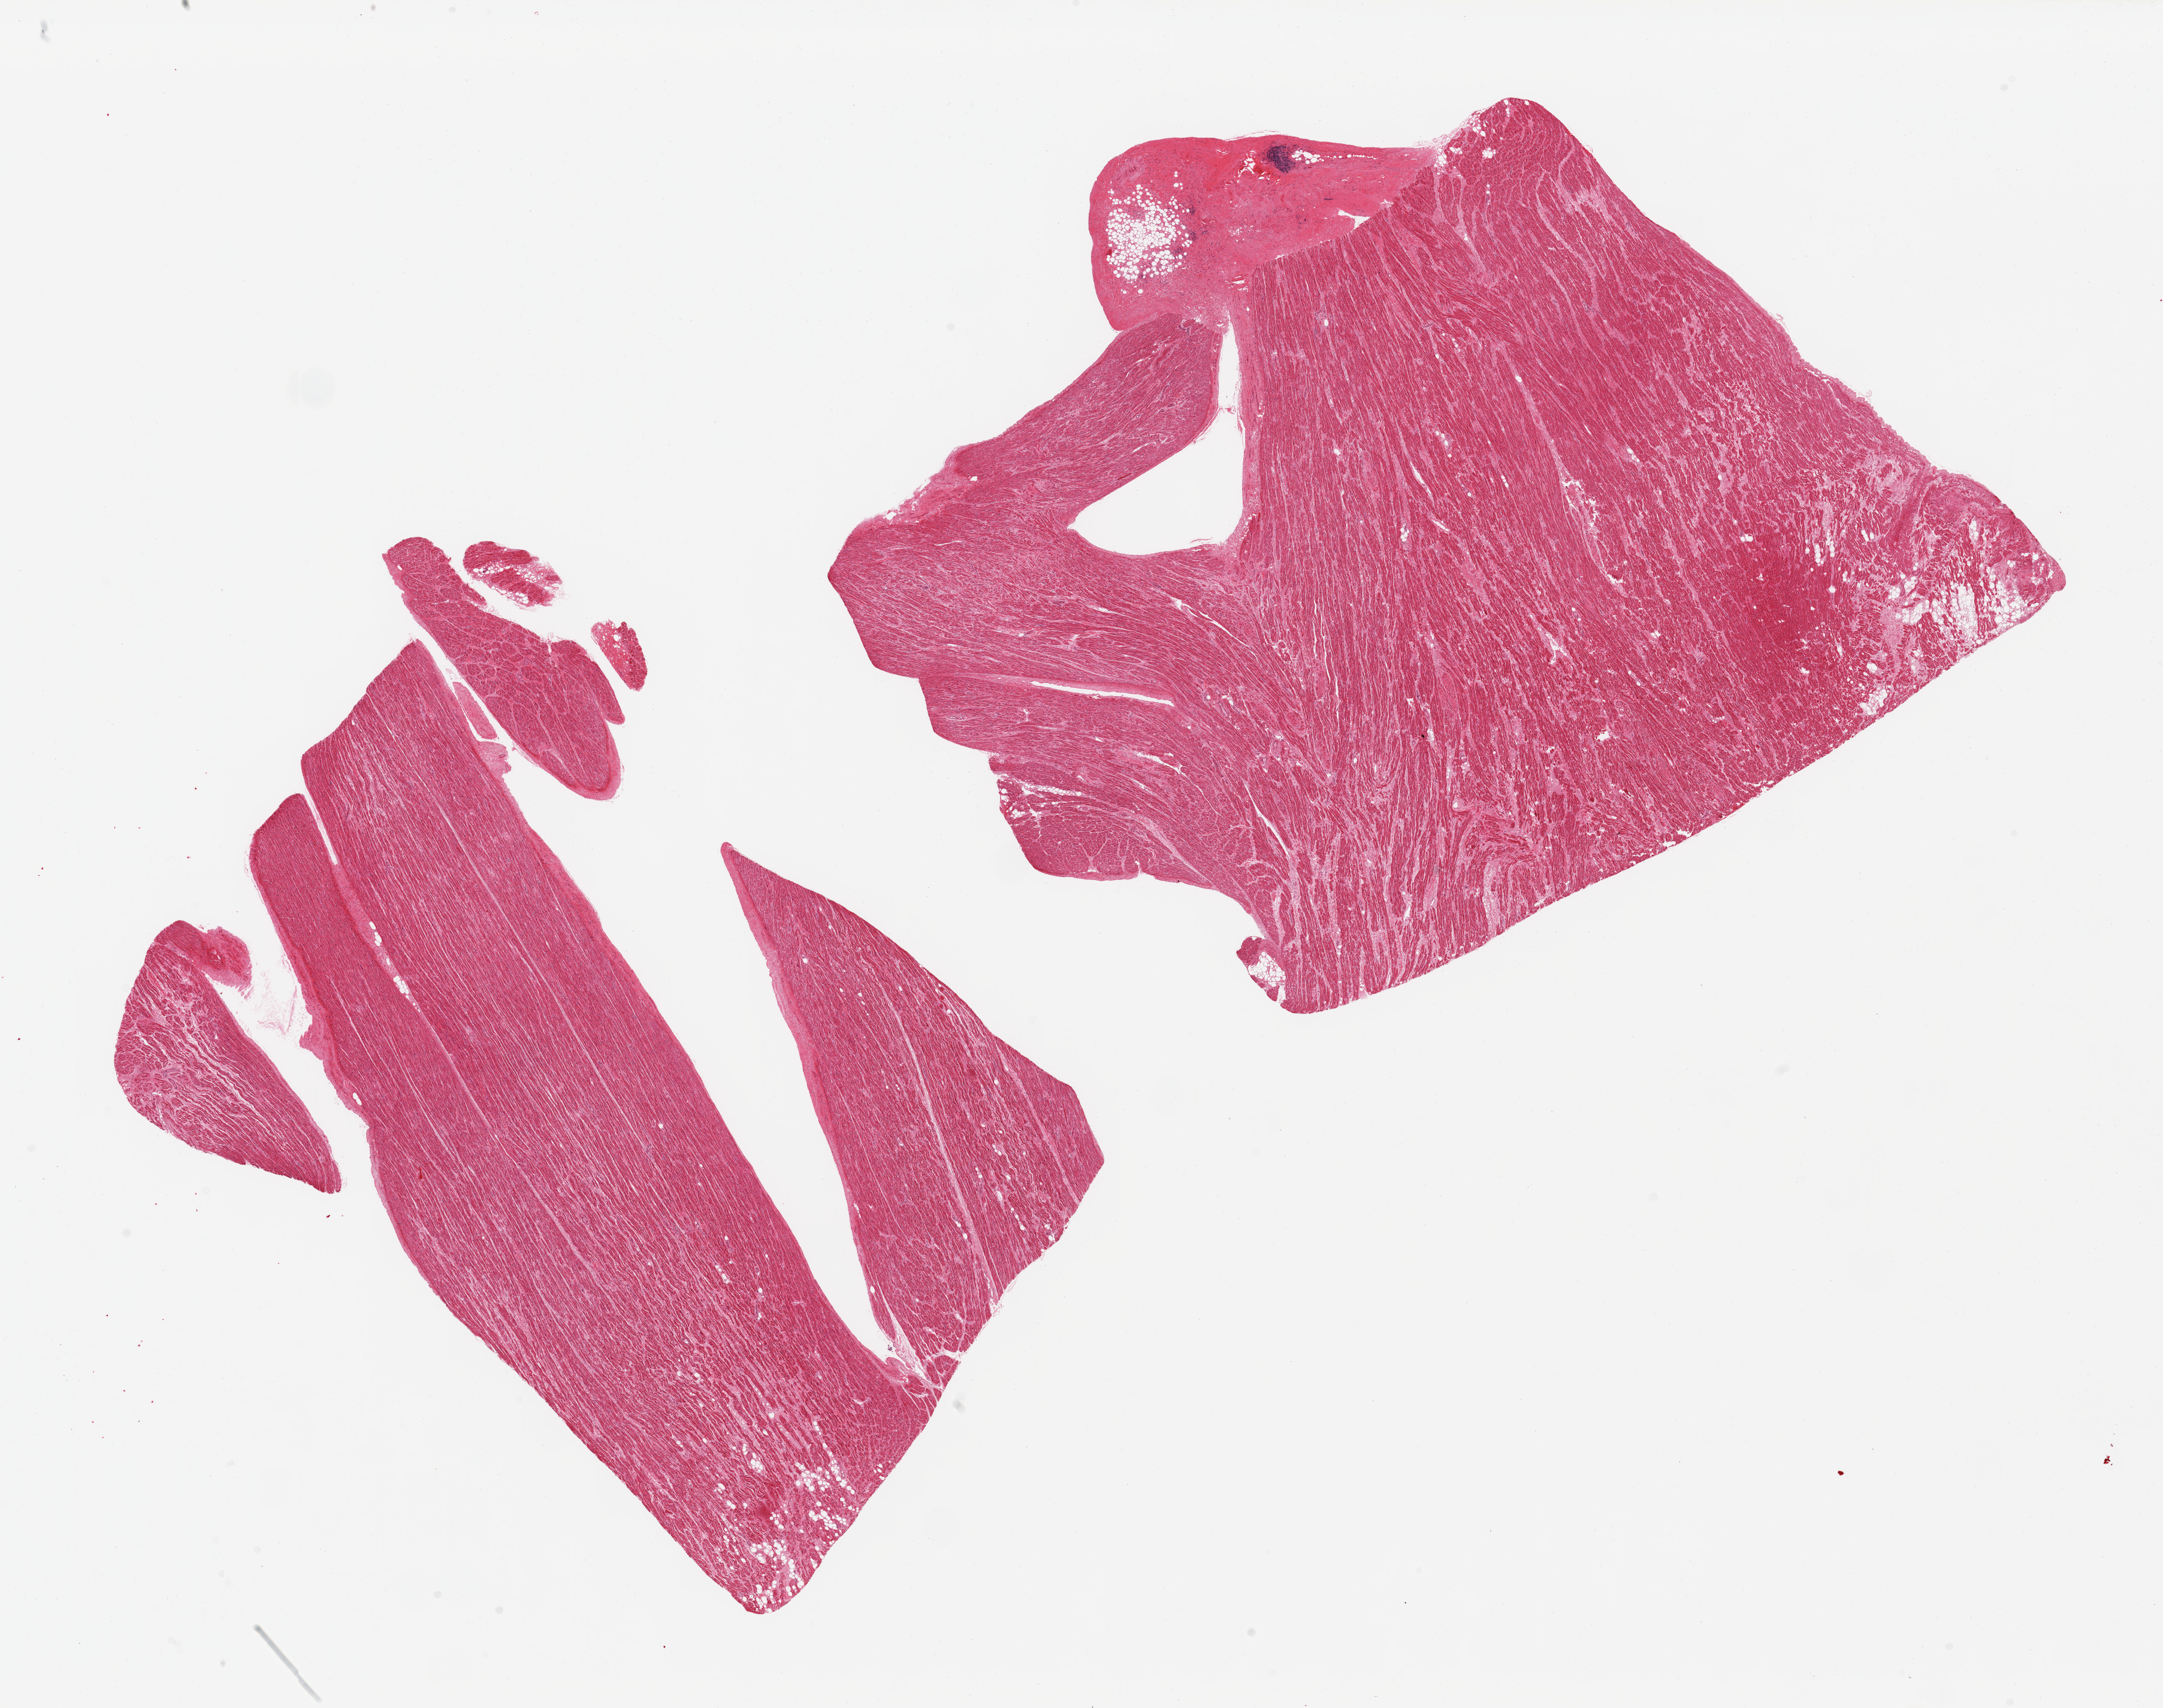
Whole-slide image, hematoxylin and eosin (H&E) stain, brightfield — whole scanned area (about 28.5 x 22.5 mm, from a 20x scan) shown as a low-resolution overview. PAXgene-fixed, paraffin-embedded tissue. Sampled site (target tissue): auricular appendage. Tissue donor sample. Male donor.
- review note (as recorded): 2 pieces; 1 focus of fibrofatty tissue 15%